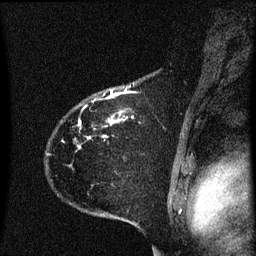
Breast MRI (dynamic contrast-enhanced), one sagittal slice; slice 50 of 60 in the series (ordered by position); dynamic contrast-enhanced series, image 2 of 3 at this slice position (ordered by acquisition); 1.5 T; TE 4.2 ms, TR 8.4 ms; 256 × 256 image matrix, field of view 200 × 200 mm. Patient: female, 35 years. From the clinical record (not read from this slice): setting: breast cancer imaged before/during neoadjuvant chemotherapy; receptor status: HER2-positive.
Structures marked on this image (semi-automatic segmentation, software-assisted and operator-edited):
- analysis volume of interest (the breast-tissue region the enhancement analysis was run in; not a lesion): bounding box <48,68,174,173> (left, top, right, bottom; pixels)
- tumour enhancement mask (voxels above the 70 % enhancement threshold inside the analysis volume of interest): <79,90,127,149>